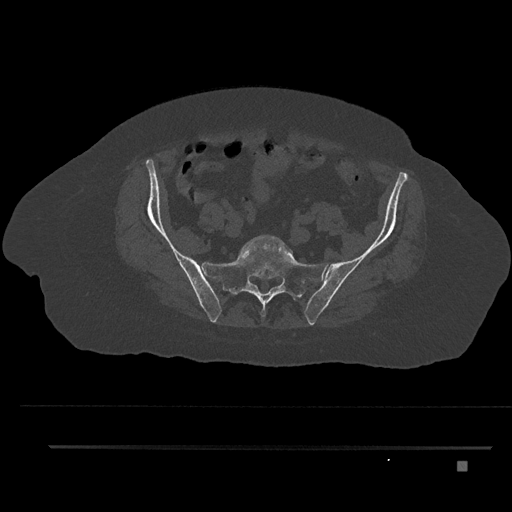
CT including the spine, one axial slice. Position 2 of 797 along the scan axis. Reconstruction kernel Br40s/3. 120 kVp. Bone window (W 1800 / L 400 HU). 0.5 mm slice thickness. 512 × 512 image matrix. Female patient, age 76 years. From the clinical record (not read from this slice): primary cancer: lung; vertebrae with lytic lesions (as recorded): T11, L3.
Outlined on this slice (semi-automatically segmented with operator editing):
- L5 vertebra: bounding box <242,235,294,260> (left, top, right, bottom; pixels)